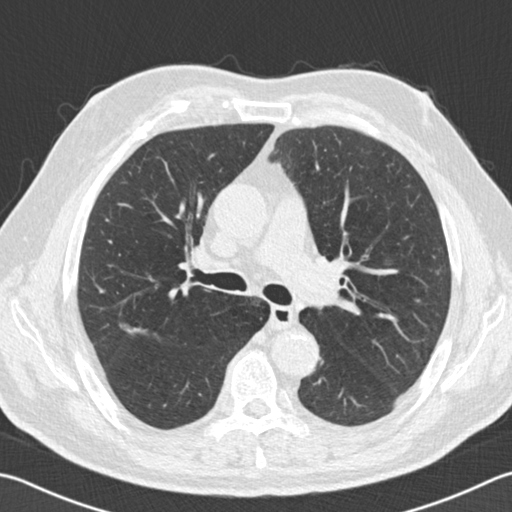
Low-dose screening chest CT, one axial slice; slice 105 of 162 in the series (ordered by position); 120 kVp; lung window (W 1500 / L -600 HU); 2 mm slice thickness; 512 × 512 image matrix, field of view 346 × 346 mm.
Outlined on this slice (manually delineated by an expert):
- lesion 1 (tumor, upper lobe of right lung): bounding box (x1, y1, x2, y2) in pixels: (119, 322, 147, 334)